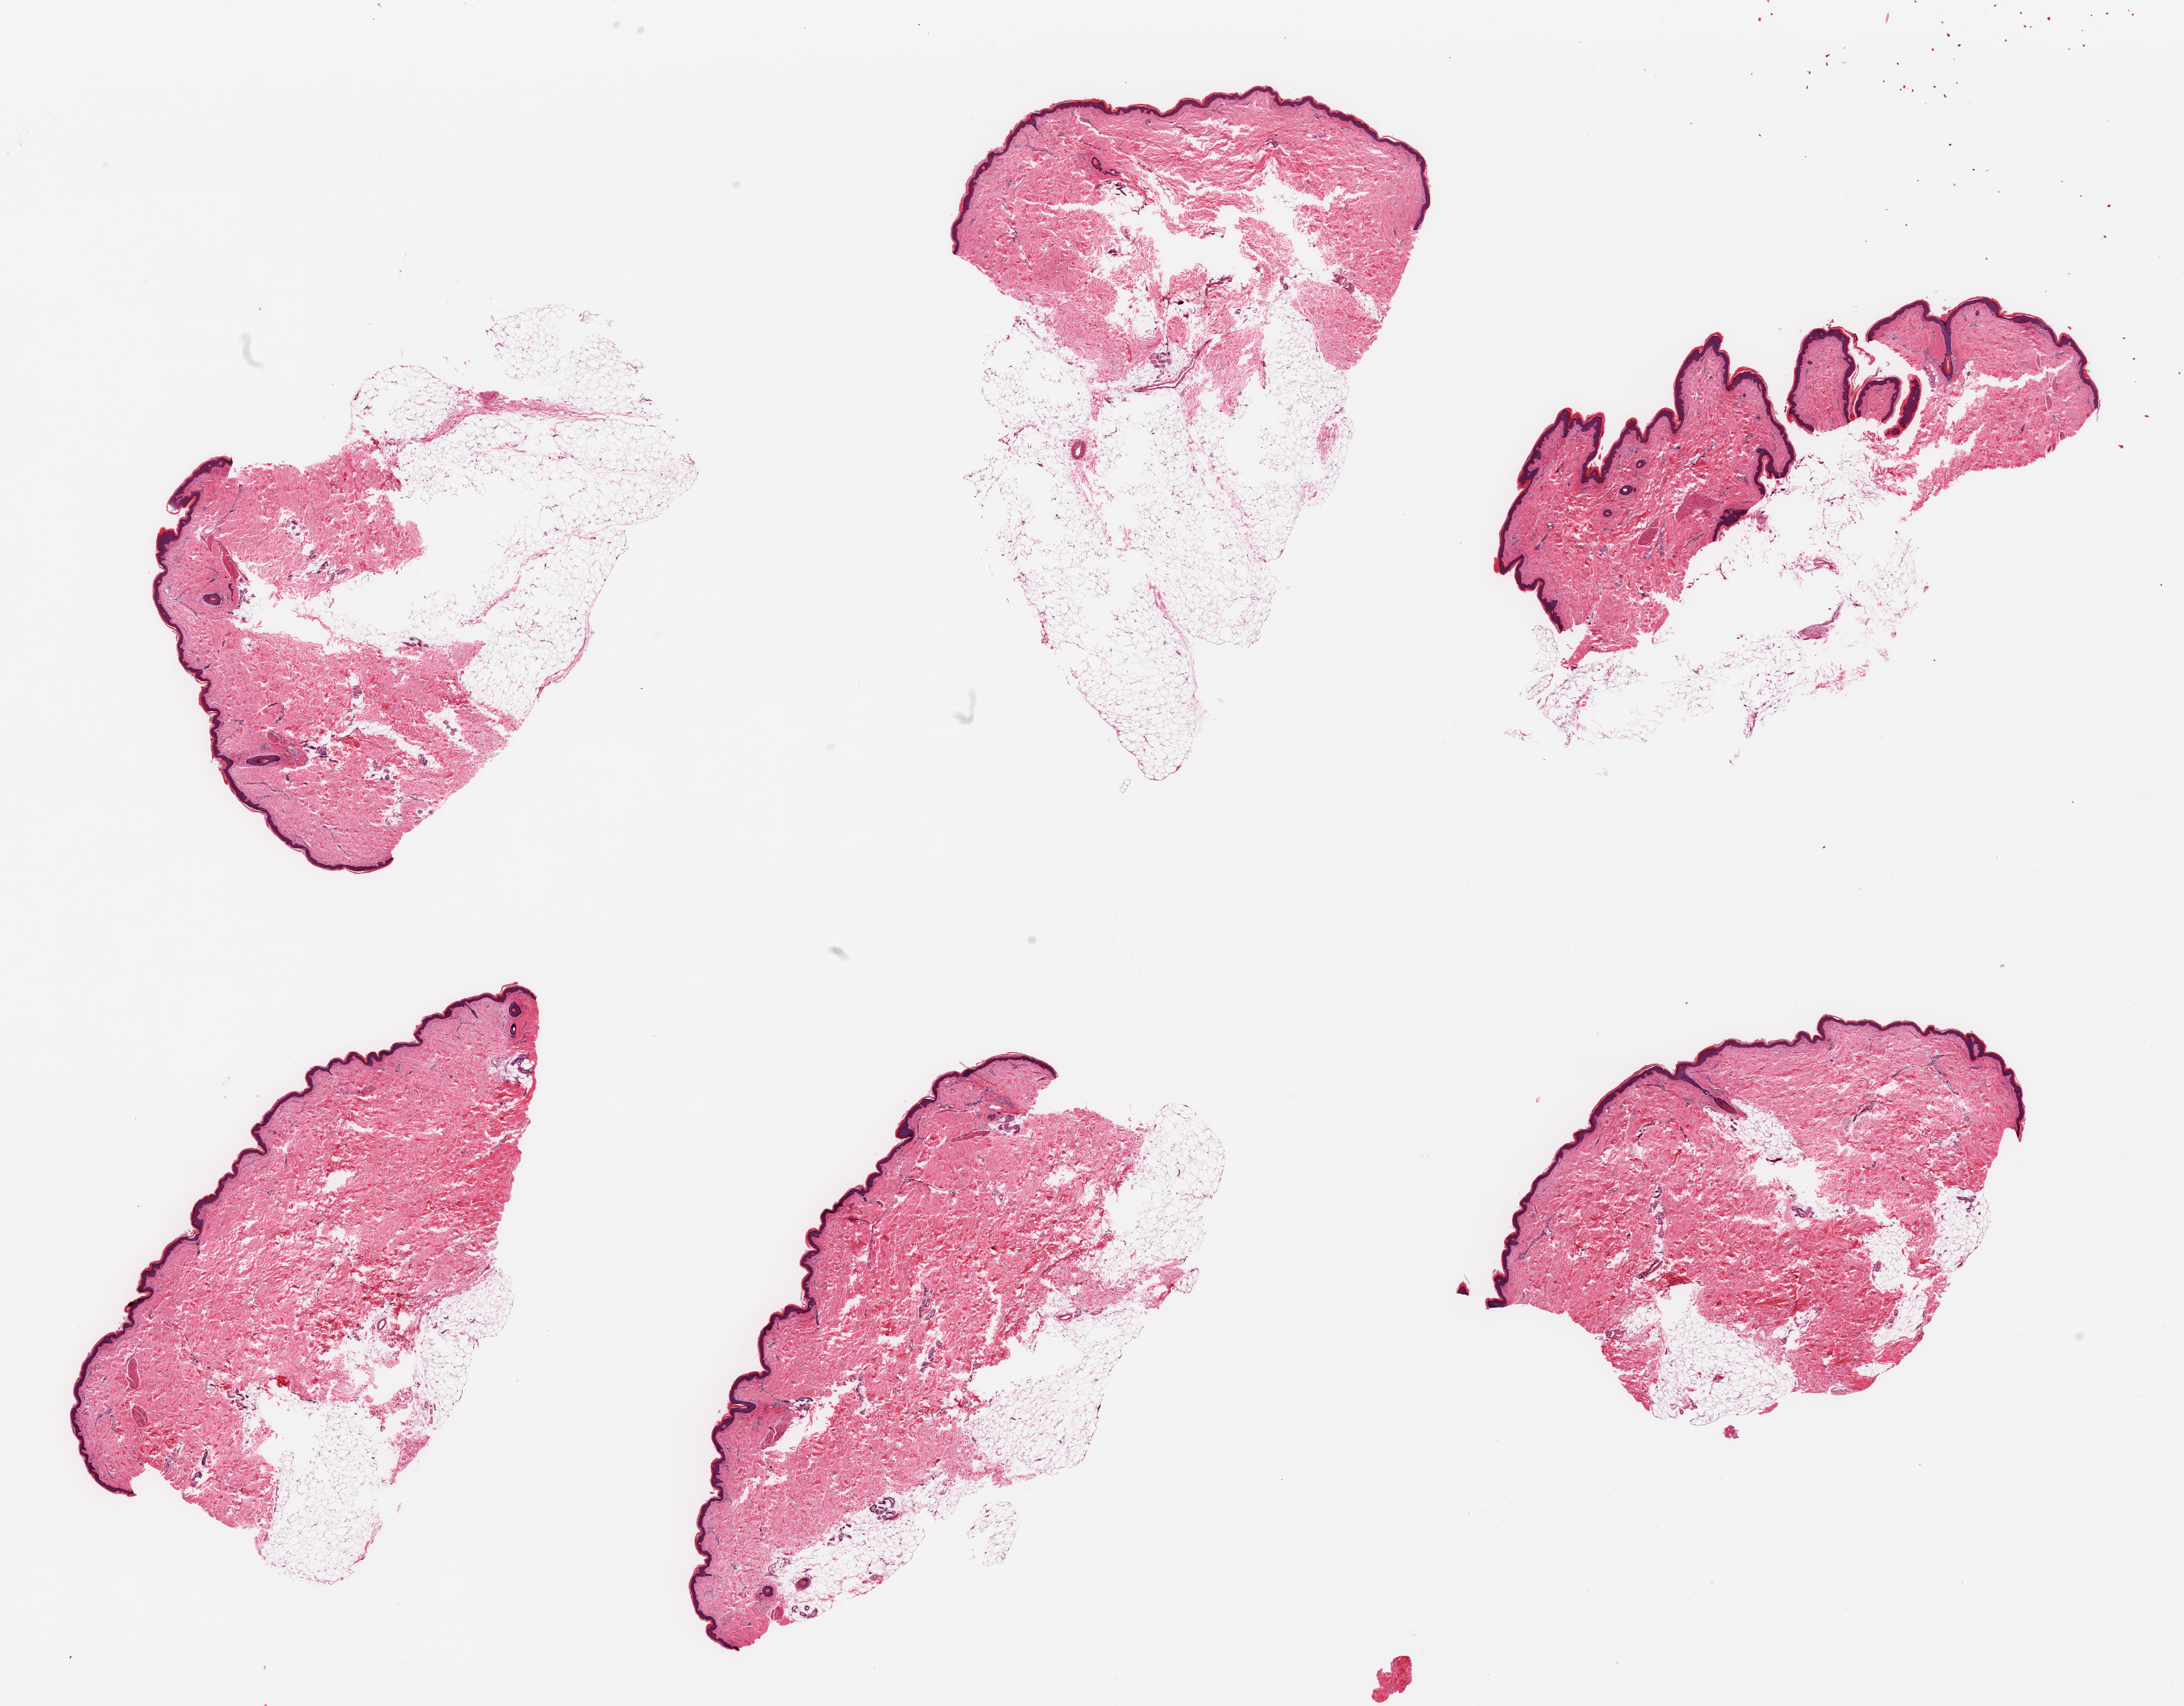
Haematoxylin and eosin whole-slide image, shown as a low-resolution overview of the whole scanned area (about 26.6 x 20.8 mm, from a 20x scan), PAXgene-fixed paraffin-embedded (PFPE) section, target tissue: skin of lower leg, donor tissue sample. Donor sex: female.
- pathologist's review note for this sample: 6 pieces, squamous epithelium is ~40 microns; abundant dermal fat up to ~4.5mm